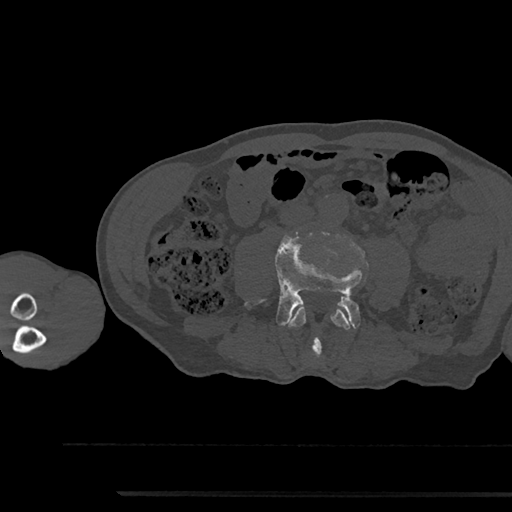
CT including the spine, one axial slice; position 440 of 797 along the scan axis; 120 kVp; bone window (W 1800 / L 400 HU); 512 × 512 image matrix, field of view 367 × 367 mm. Male patient, age 79 years. From the clinical record (not read from this slice): primary cancer: prostate.
Outlined on this slice (semi-automatically segmented with operator editing):
- L3 vertebra: box from (x=288, y=304) to (x=351, y=356) px
- L4 vertebra: (x=246, y=236)–(x=362, y=329)